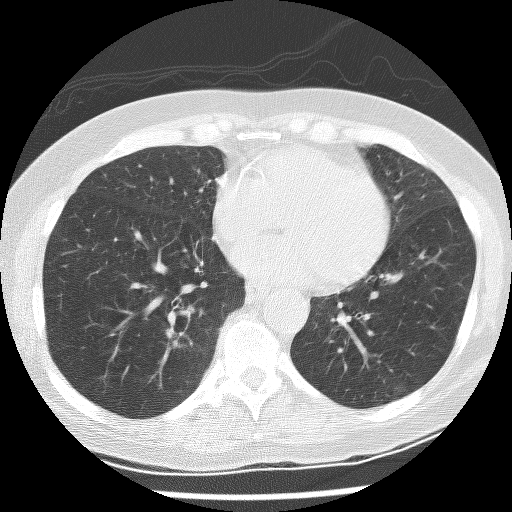
Low-dose screening chest CT, one axial slice; position 97 of 247 along the scan axis; reconstruction kernel BONE; 120 kVp; lung window (W 1500 / L -600 HU); 512 × 512 image matrix.
Annotated regions visible in this slice (outlined manually by an expert reader):
- lesion 1 (tumor, lower lobe of right lung): bounding box [x1, y1, x2, y2] px = [166, 327, 186, 350]